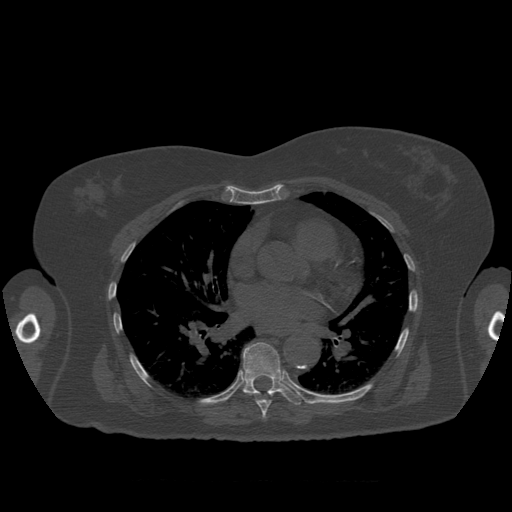
CT including the spine, one axial slice. Slice 387 of 399 in the series (ordered by position). Reconstruction kernel STANDARD. 120 kVp. Bone window (W 1800 / L 400 HU). 1.25 mm slice thickness. 512 × 512 image matrix, field of view 404 × 404 mm. Patient age 81 years. Case-level facts recorded for this patient, not image findings: primary cancer: renal; vertebrae with lytic lesions (as recorded): L1.
Structures marked on this image (semi-automatically segmented with operator editing):
- T7 vertebra: bounding box [x1, y1, x2, y2] px = [243, 391, 274, 418]
- T8 vertebra: [242, 343, 304, 406]